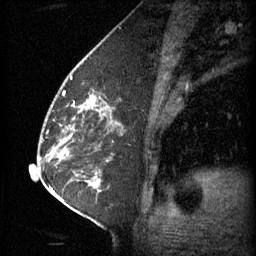
Breast MRI (dynamic contrast-enhanced), one sagittal slice; position 30 of 60 along the scan axis; 3 images stored at this slice position (order not interpretable as contrast timing); 1.5 T; TE 4.2 ms, TR 11 ms; 256 × 256 image matrix. Patient: female, 62 years.
Outlined on this slice (semi-automatic segmentation, software-assisted and operator-edited):
- analysis volume of interest (the breast-tissue region the enhancement analysis was run in; not a lesion): box from (x=55, y=72) to (x=114, y=131) px
- tumour enhancement mask (voxels above the 70 % enhancement threshold inside the analysis volume of interest): (x=82, y=96)–(x=96, y=109)